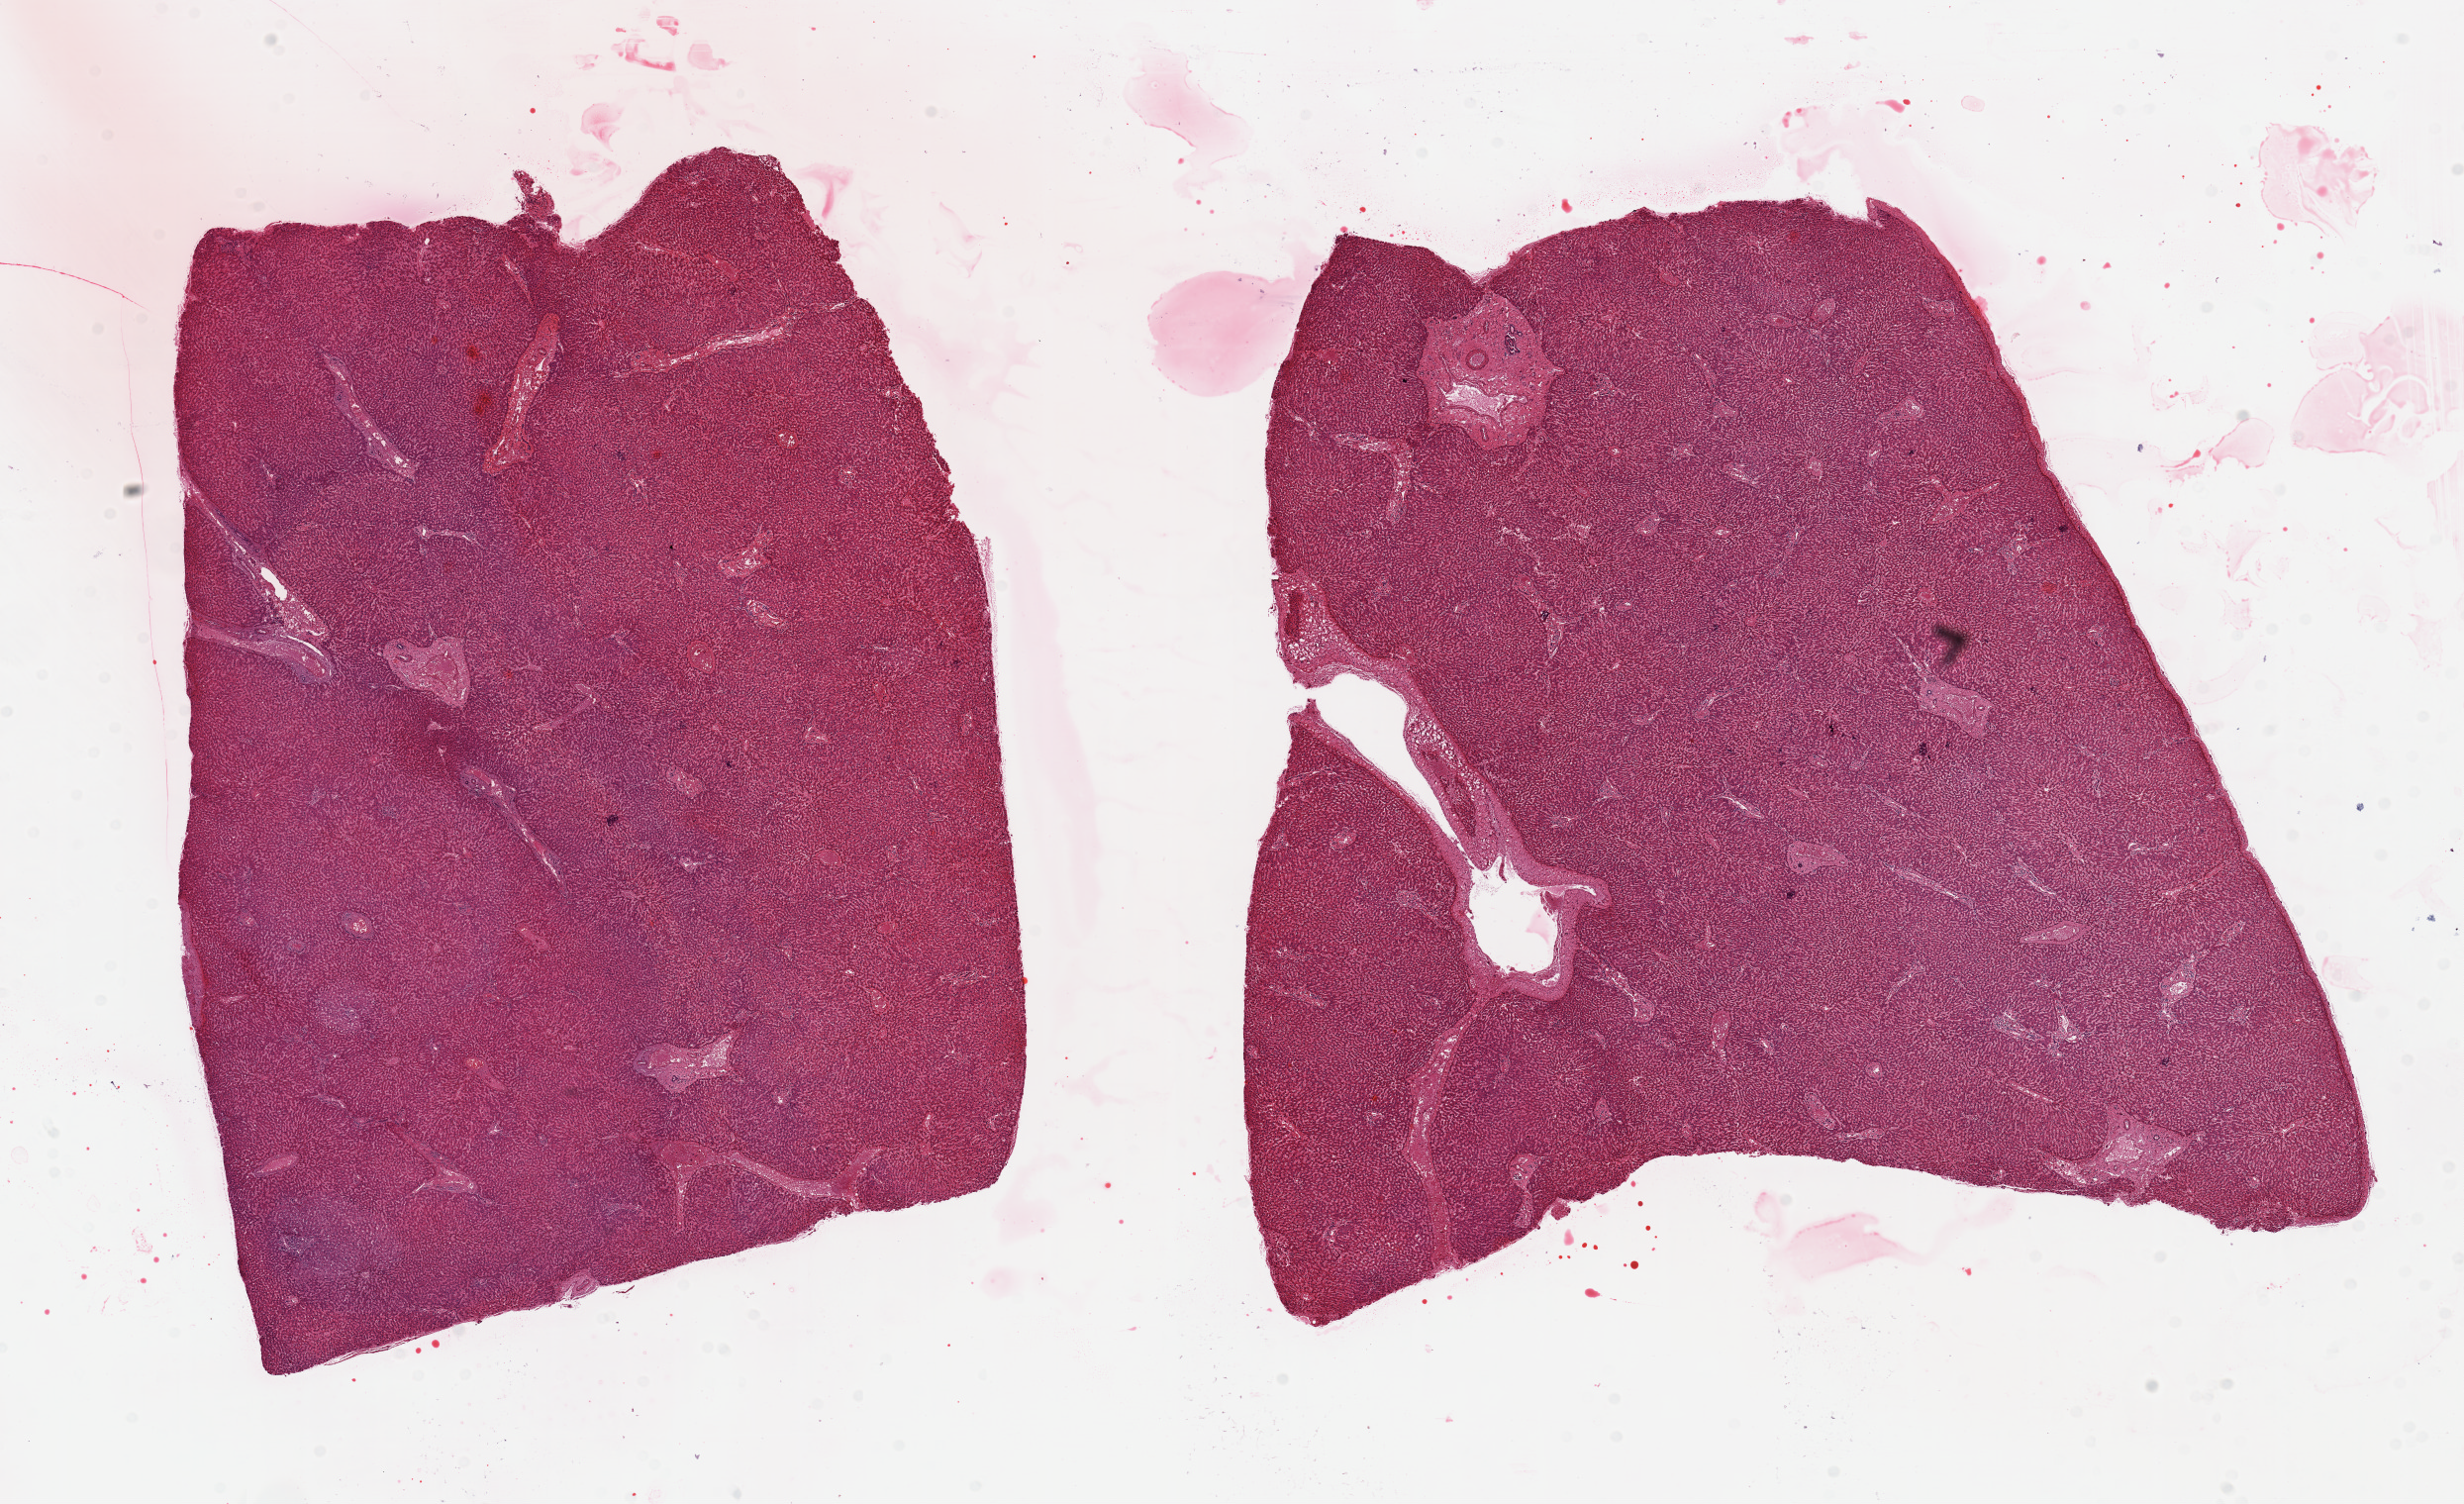
Digitized H&E-stained section, a low-resolution overview of the entire scanned area, about 19.7 x 12.0 mm (from a 20x scan), PAXgene-fixed, paraffin-embedded tissue, sampled site (target tissue): liver, tissue donor sample. Donor sex: male.
- review note (as recorded): 2 pieces, 9x7 & 9x9mm; no steatosis